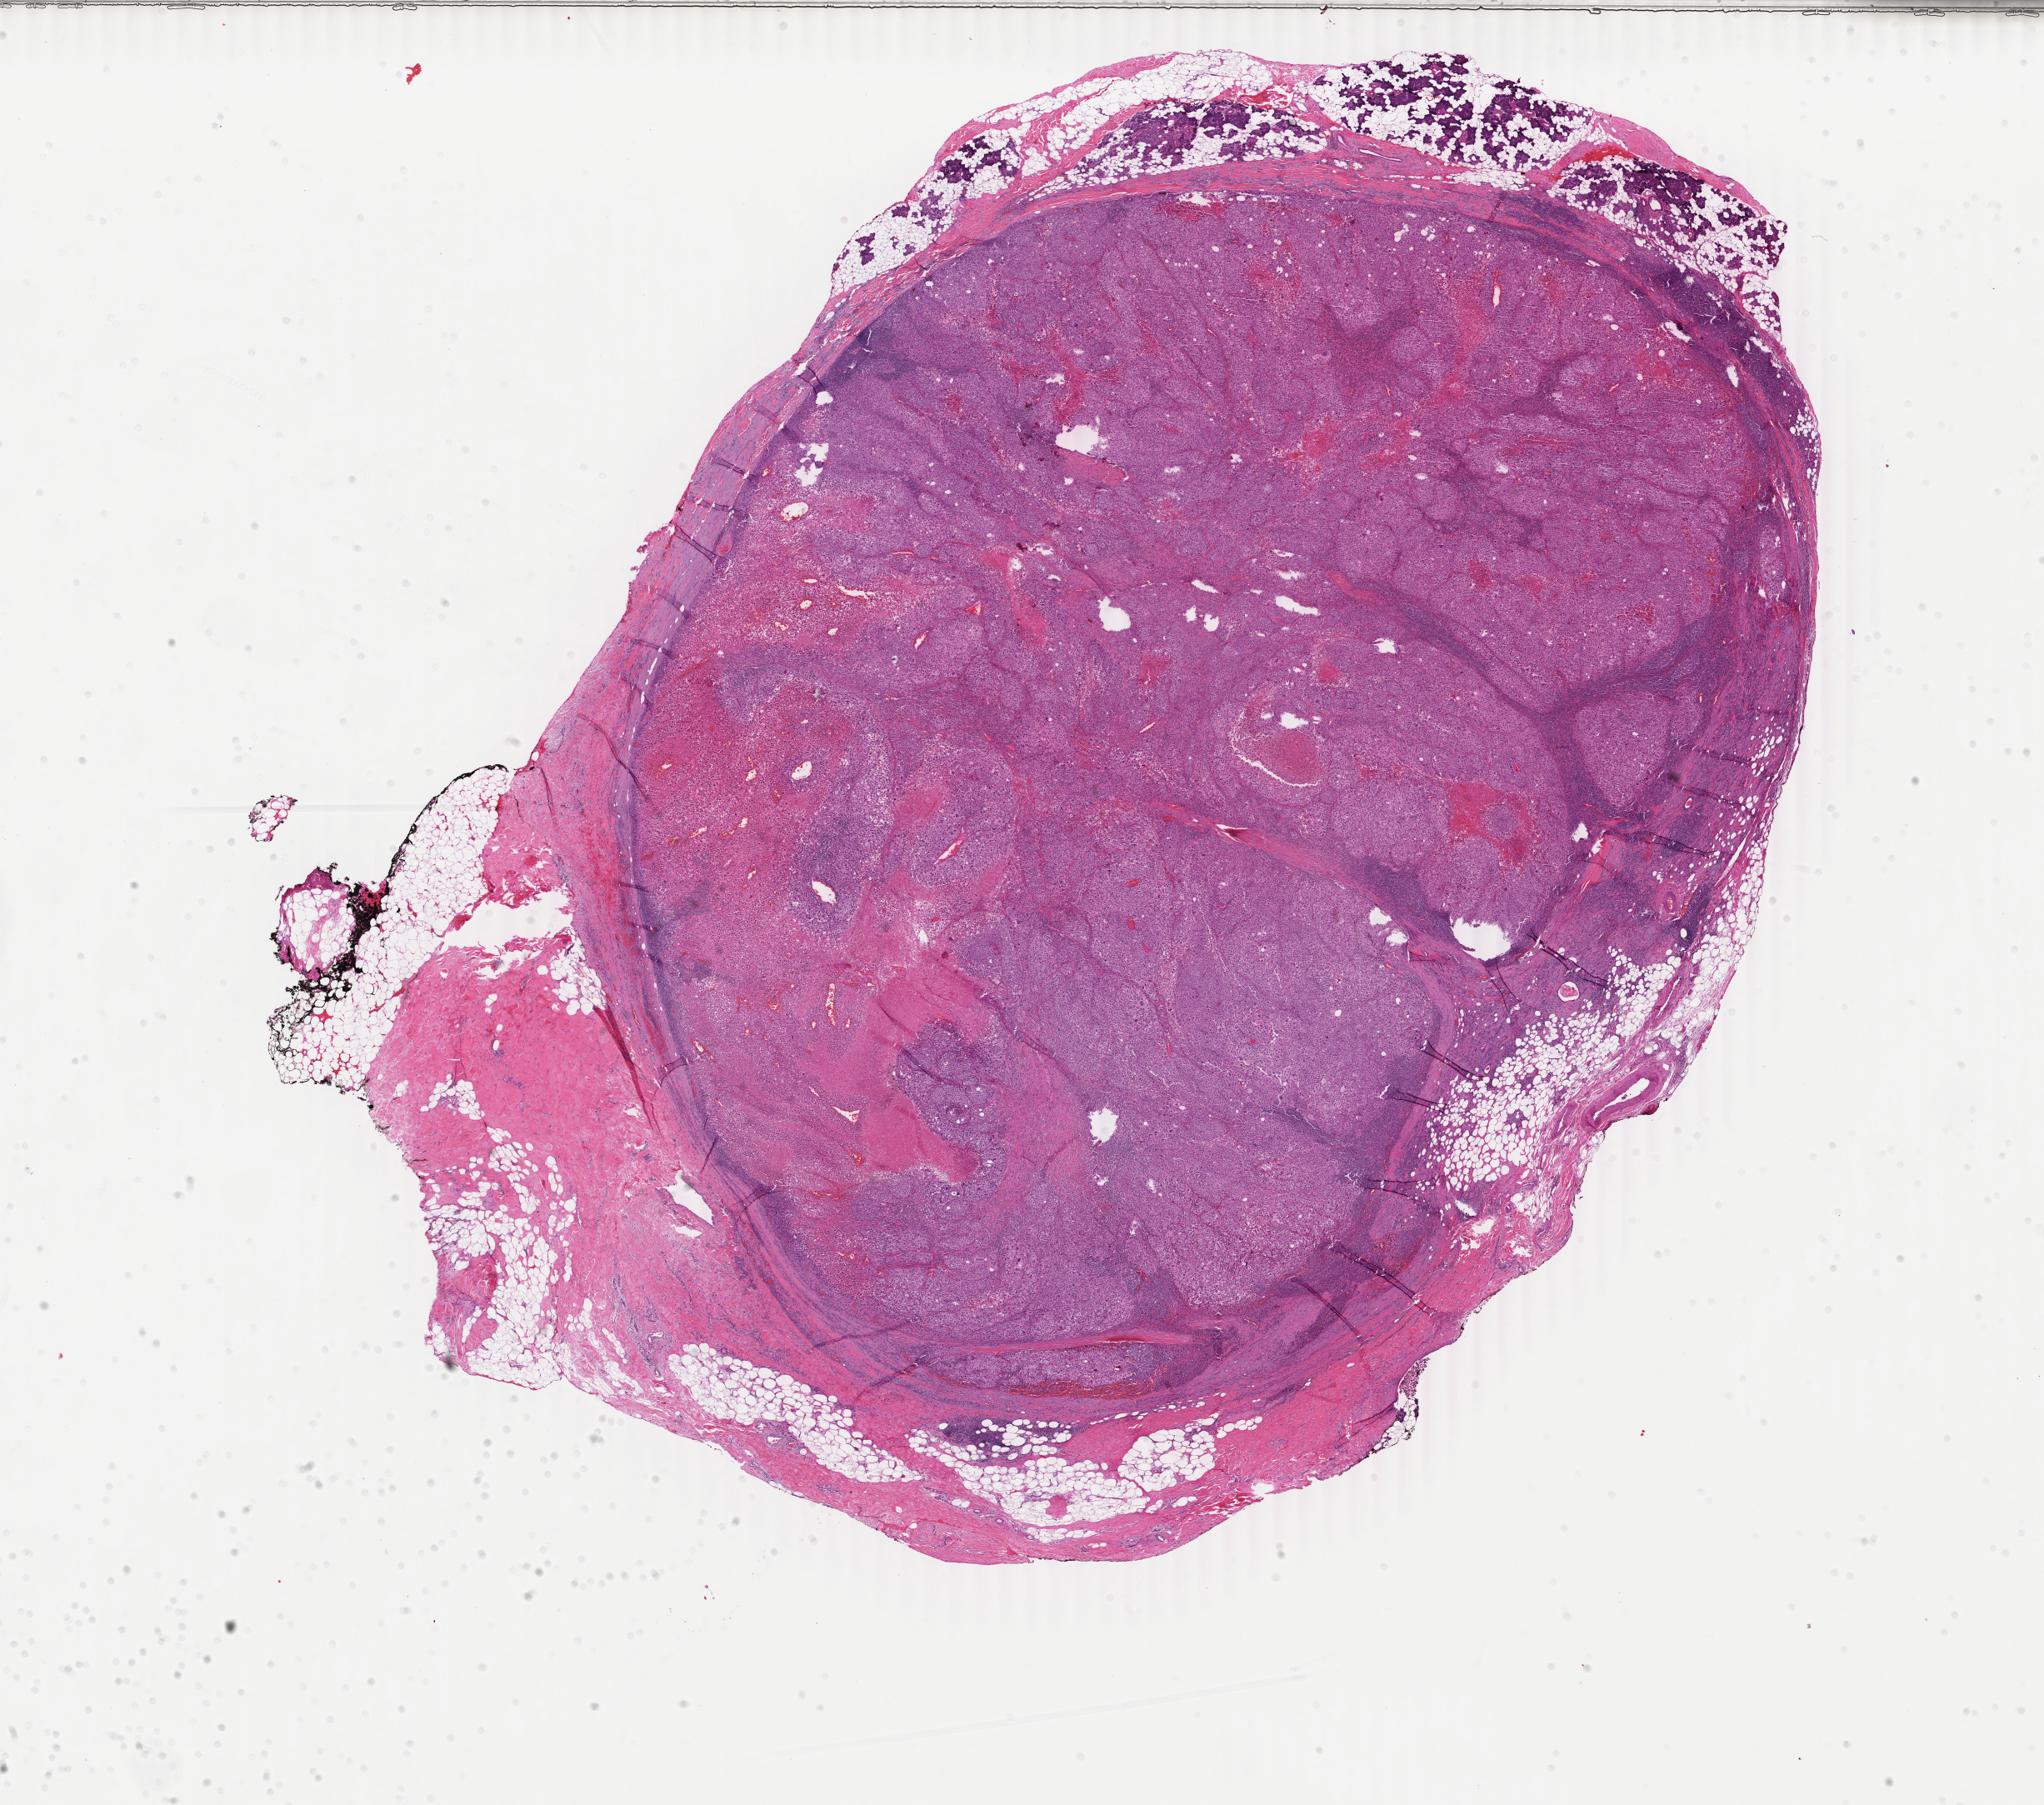
Digitized H&E-stained tissue section (whole slide), whole scanned area (about 19.5 x 17.2 mm) shown as a low-resolution overview, FFPE section, primary tumour sample from the skin. Male, age 82 years at initial diagnosis.
Pathologic diagnosis: Malignant melanoma, NOS.